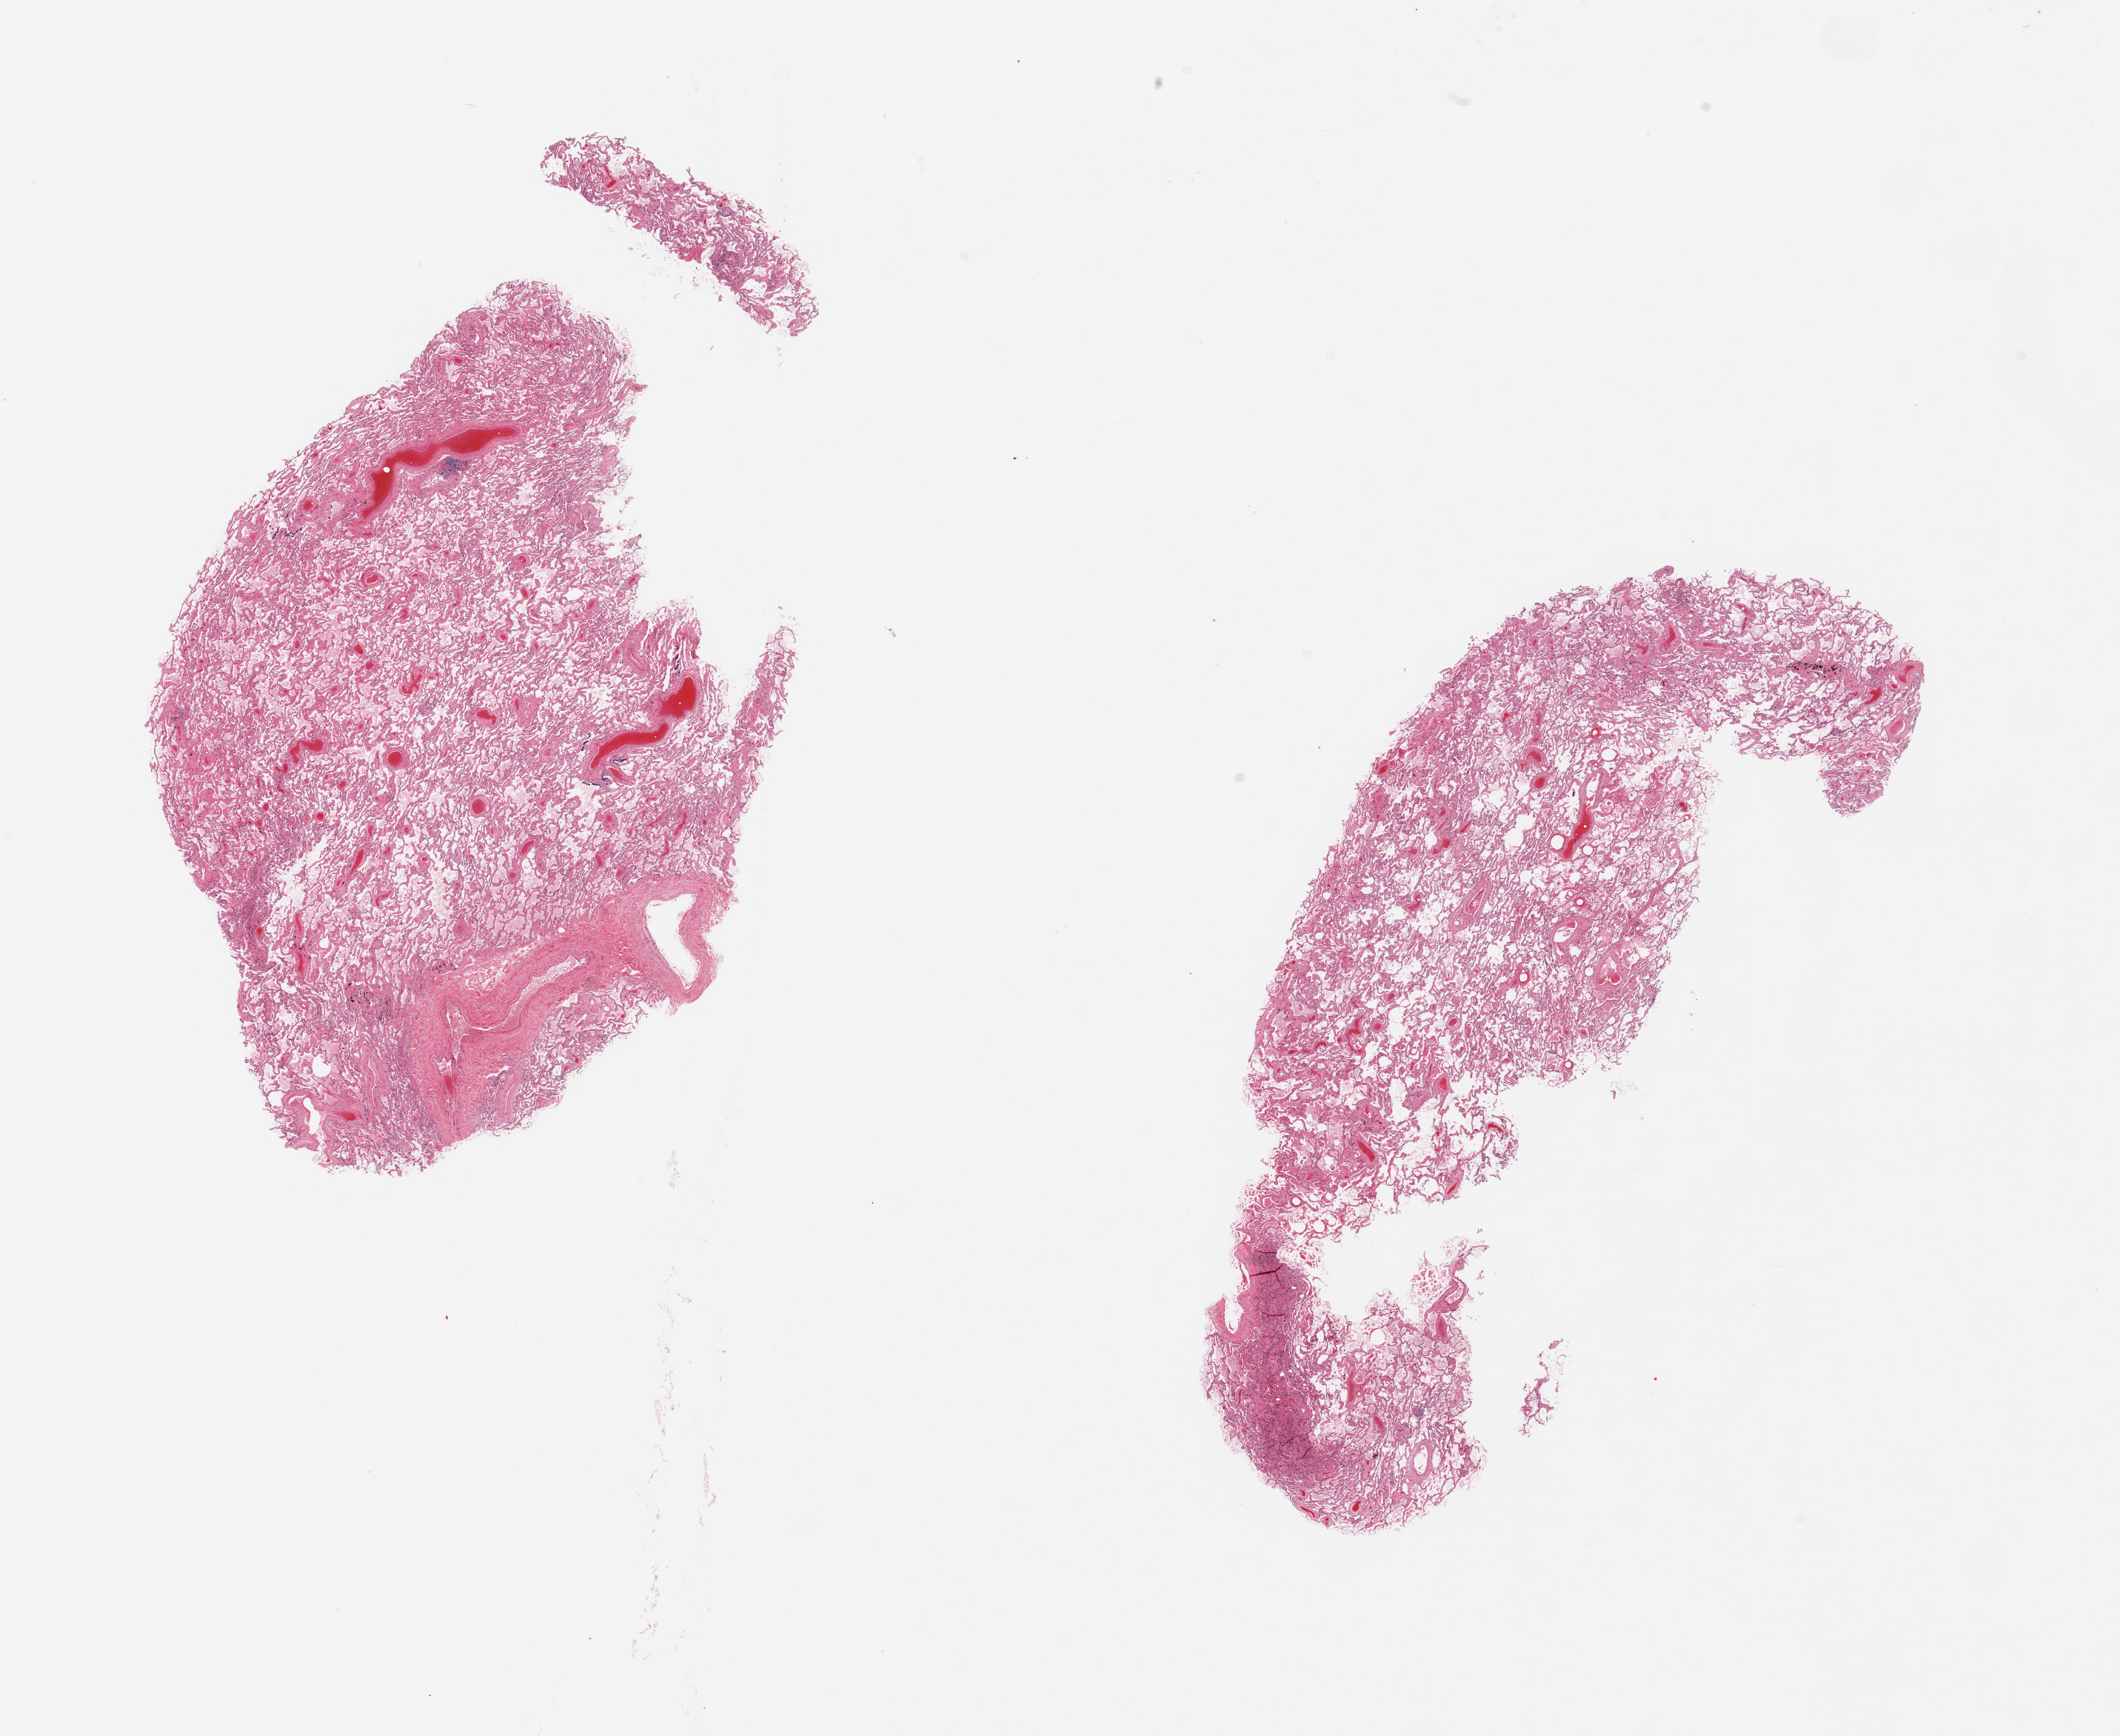
H&E whole-slide image — low-resolution overview of the scanned area, about 22.6 x 18.5 mm (slide scanned at 20x). PAXgene-fixed paraffin-embedded (PFPE) section. Target tissue: lung. Tissue donor sample. Donor: male.
• pathologist's review note for this sample: 2 pieces minimal congestion